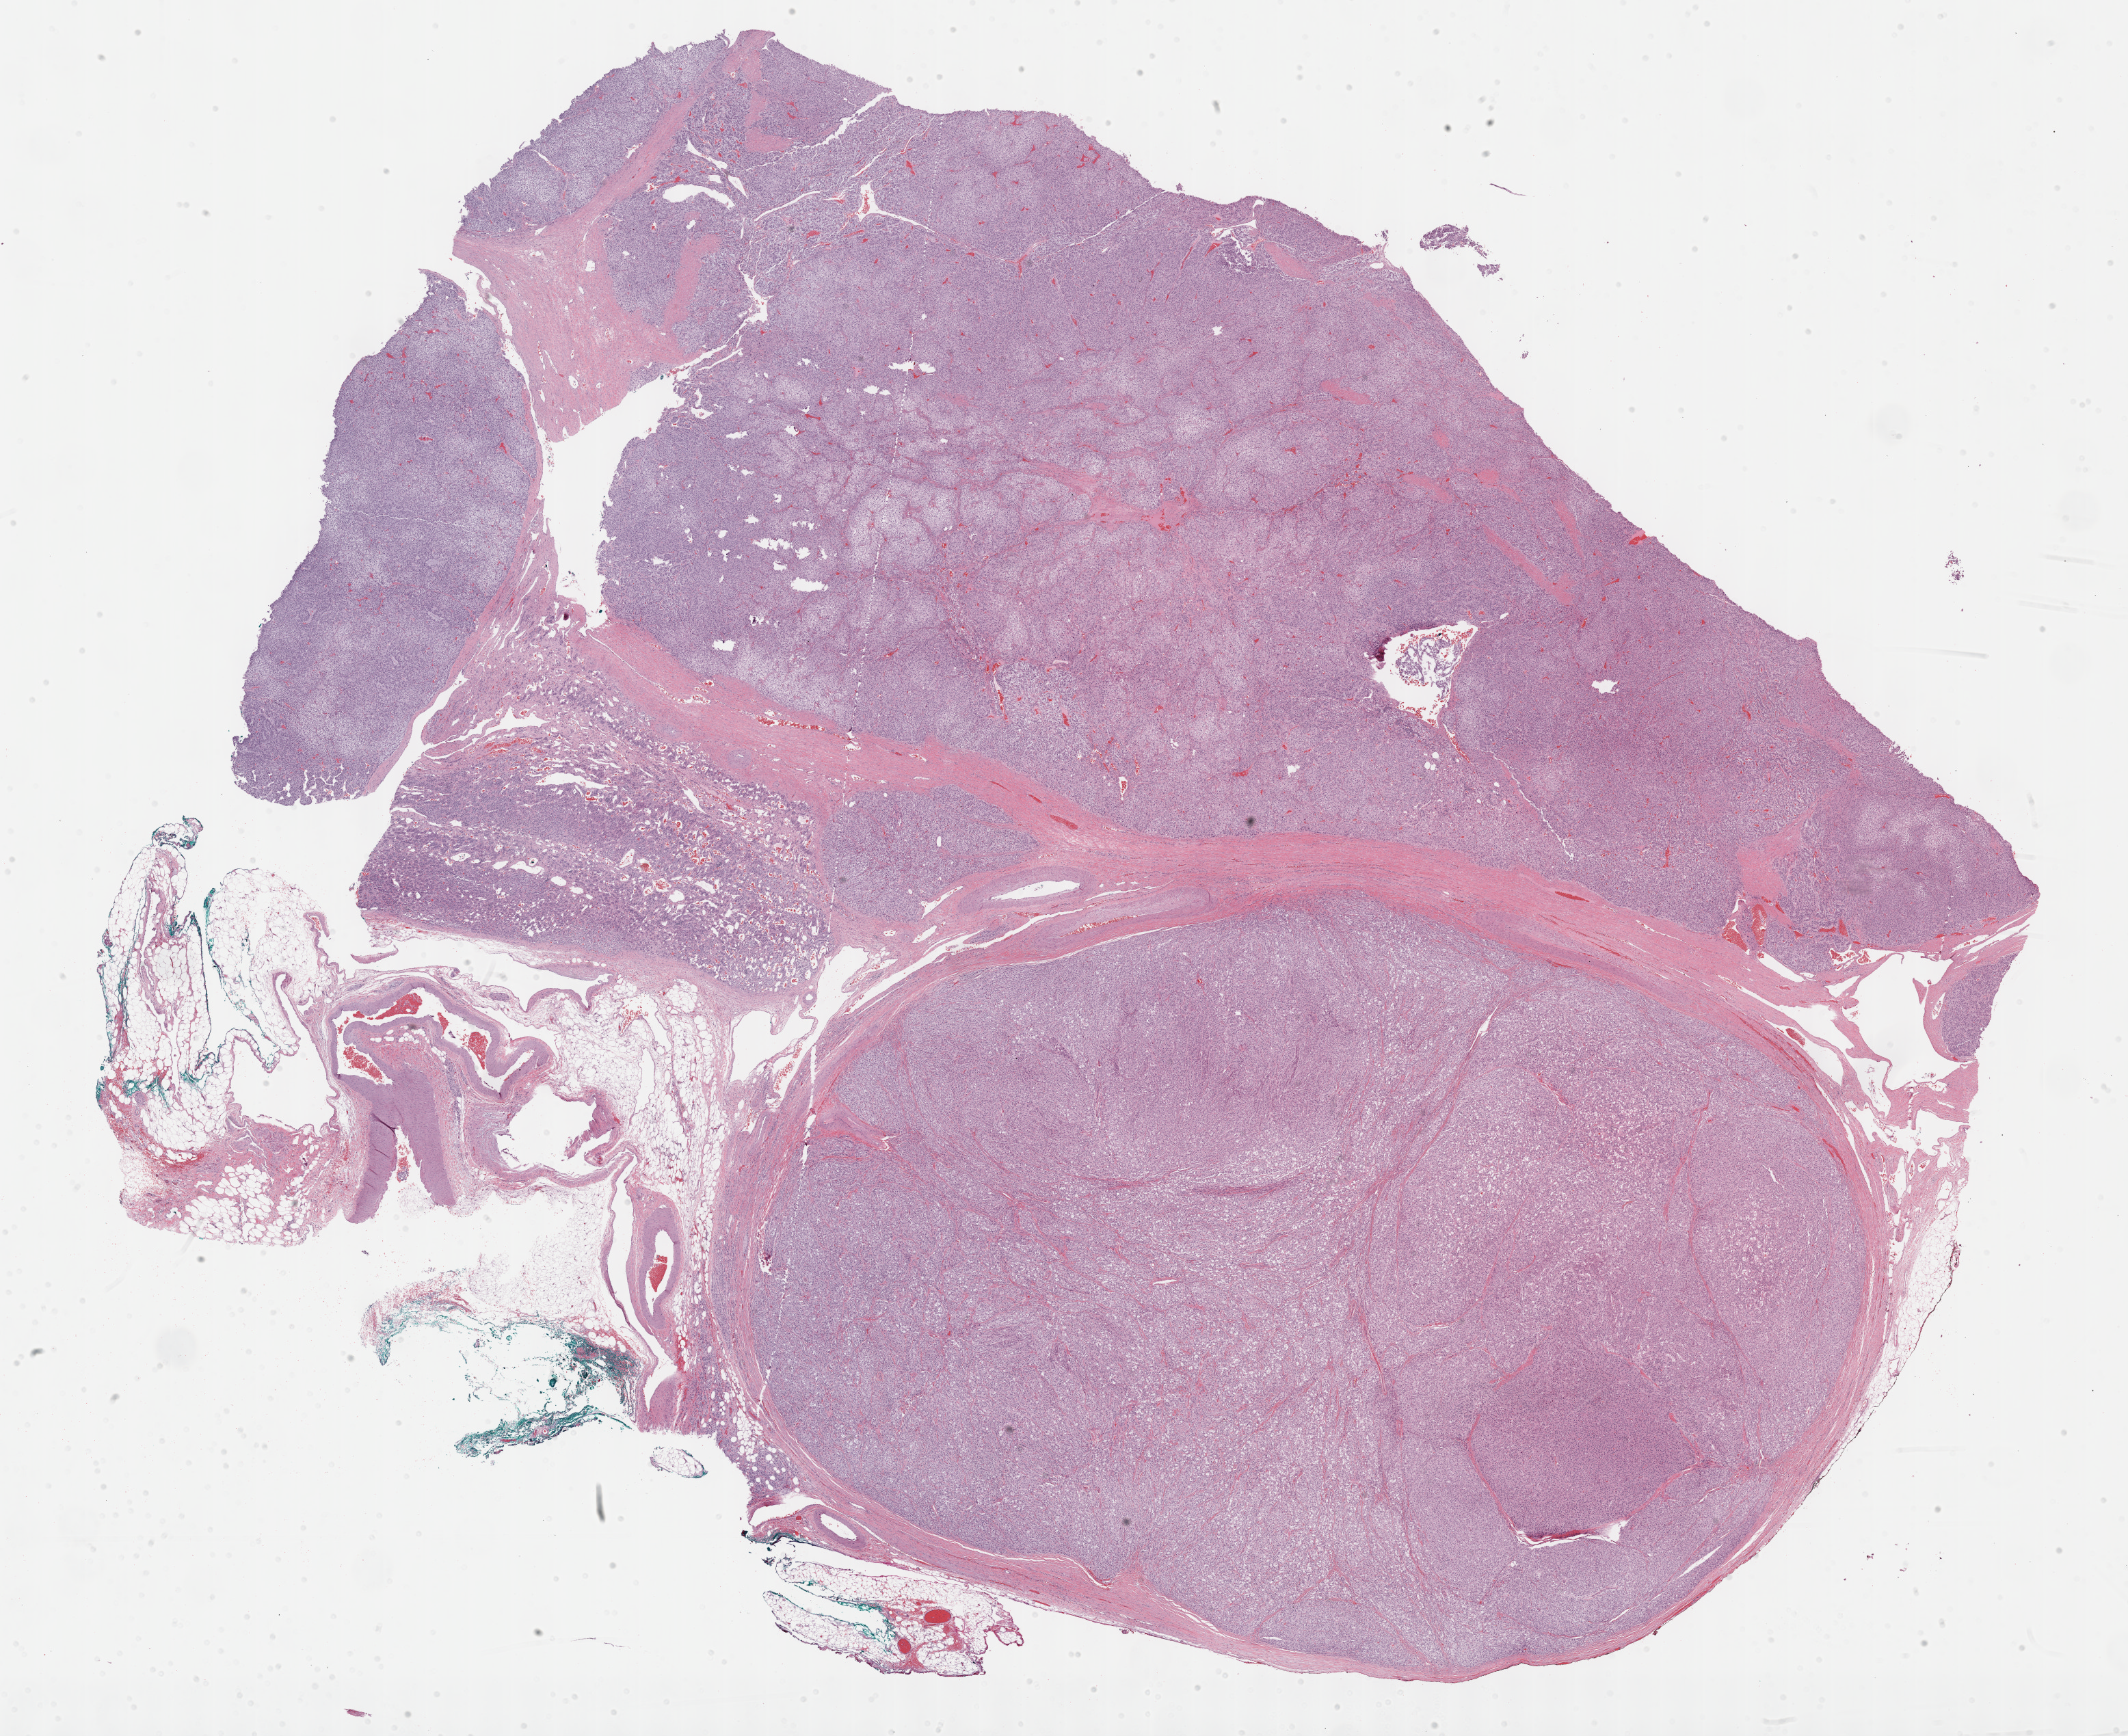
Hematoxylin and eosin (H&E) stained whole-slide image, a low-resolution overview of the entire scanned area, about 25.2 x 20.5 mm (from a 40x scan), FFPE section, sample: primary tumour, adrenal cortex. Male patient; age at initial diagnosis 50 years.
Pathologic diagnosis: Adrenal cortical carcinoma. Lymph nodes positive (case pathology): 0 of 1 examined.